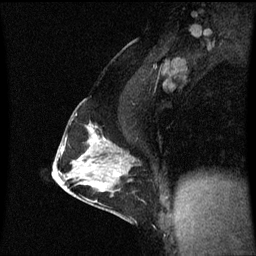
Breast MRI (dynamic contrast-enhanced), one sagittal slice; position 36 of 60 along the scan axis; dynamic contrast-enhanced series, image 2 of 3 at this slice position (ordered by acquisition); 1.5 T; TE 4.2 ms, TR 8.9 ms; 2 mm slice thickness; 256 × 256 image matrix, field of view 200 × 200 mm. Patient: female, 47 years. From the clinical record (not read from this slice): setting: breast cancer imaged before/during neoadjuvant chemotherapy; receptor status: HR-positive, HER2-negative.
Outlined on this slice (semi-automatically segmented with operator editing):
- analysis volume of interest (the breast-tissue region the enhancement analysis was run in; not a lesion): bounding box [x1, y1, x2, y2] px = [54, 110, 137, 209]
- tumour enhancement mask (voxels above the 70 % enhancement threshold inside the analysis volume of interest): [89, 128, 116, 175]